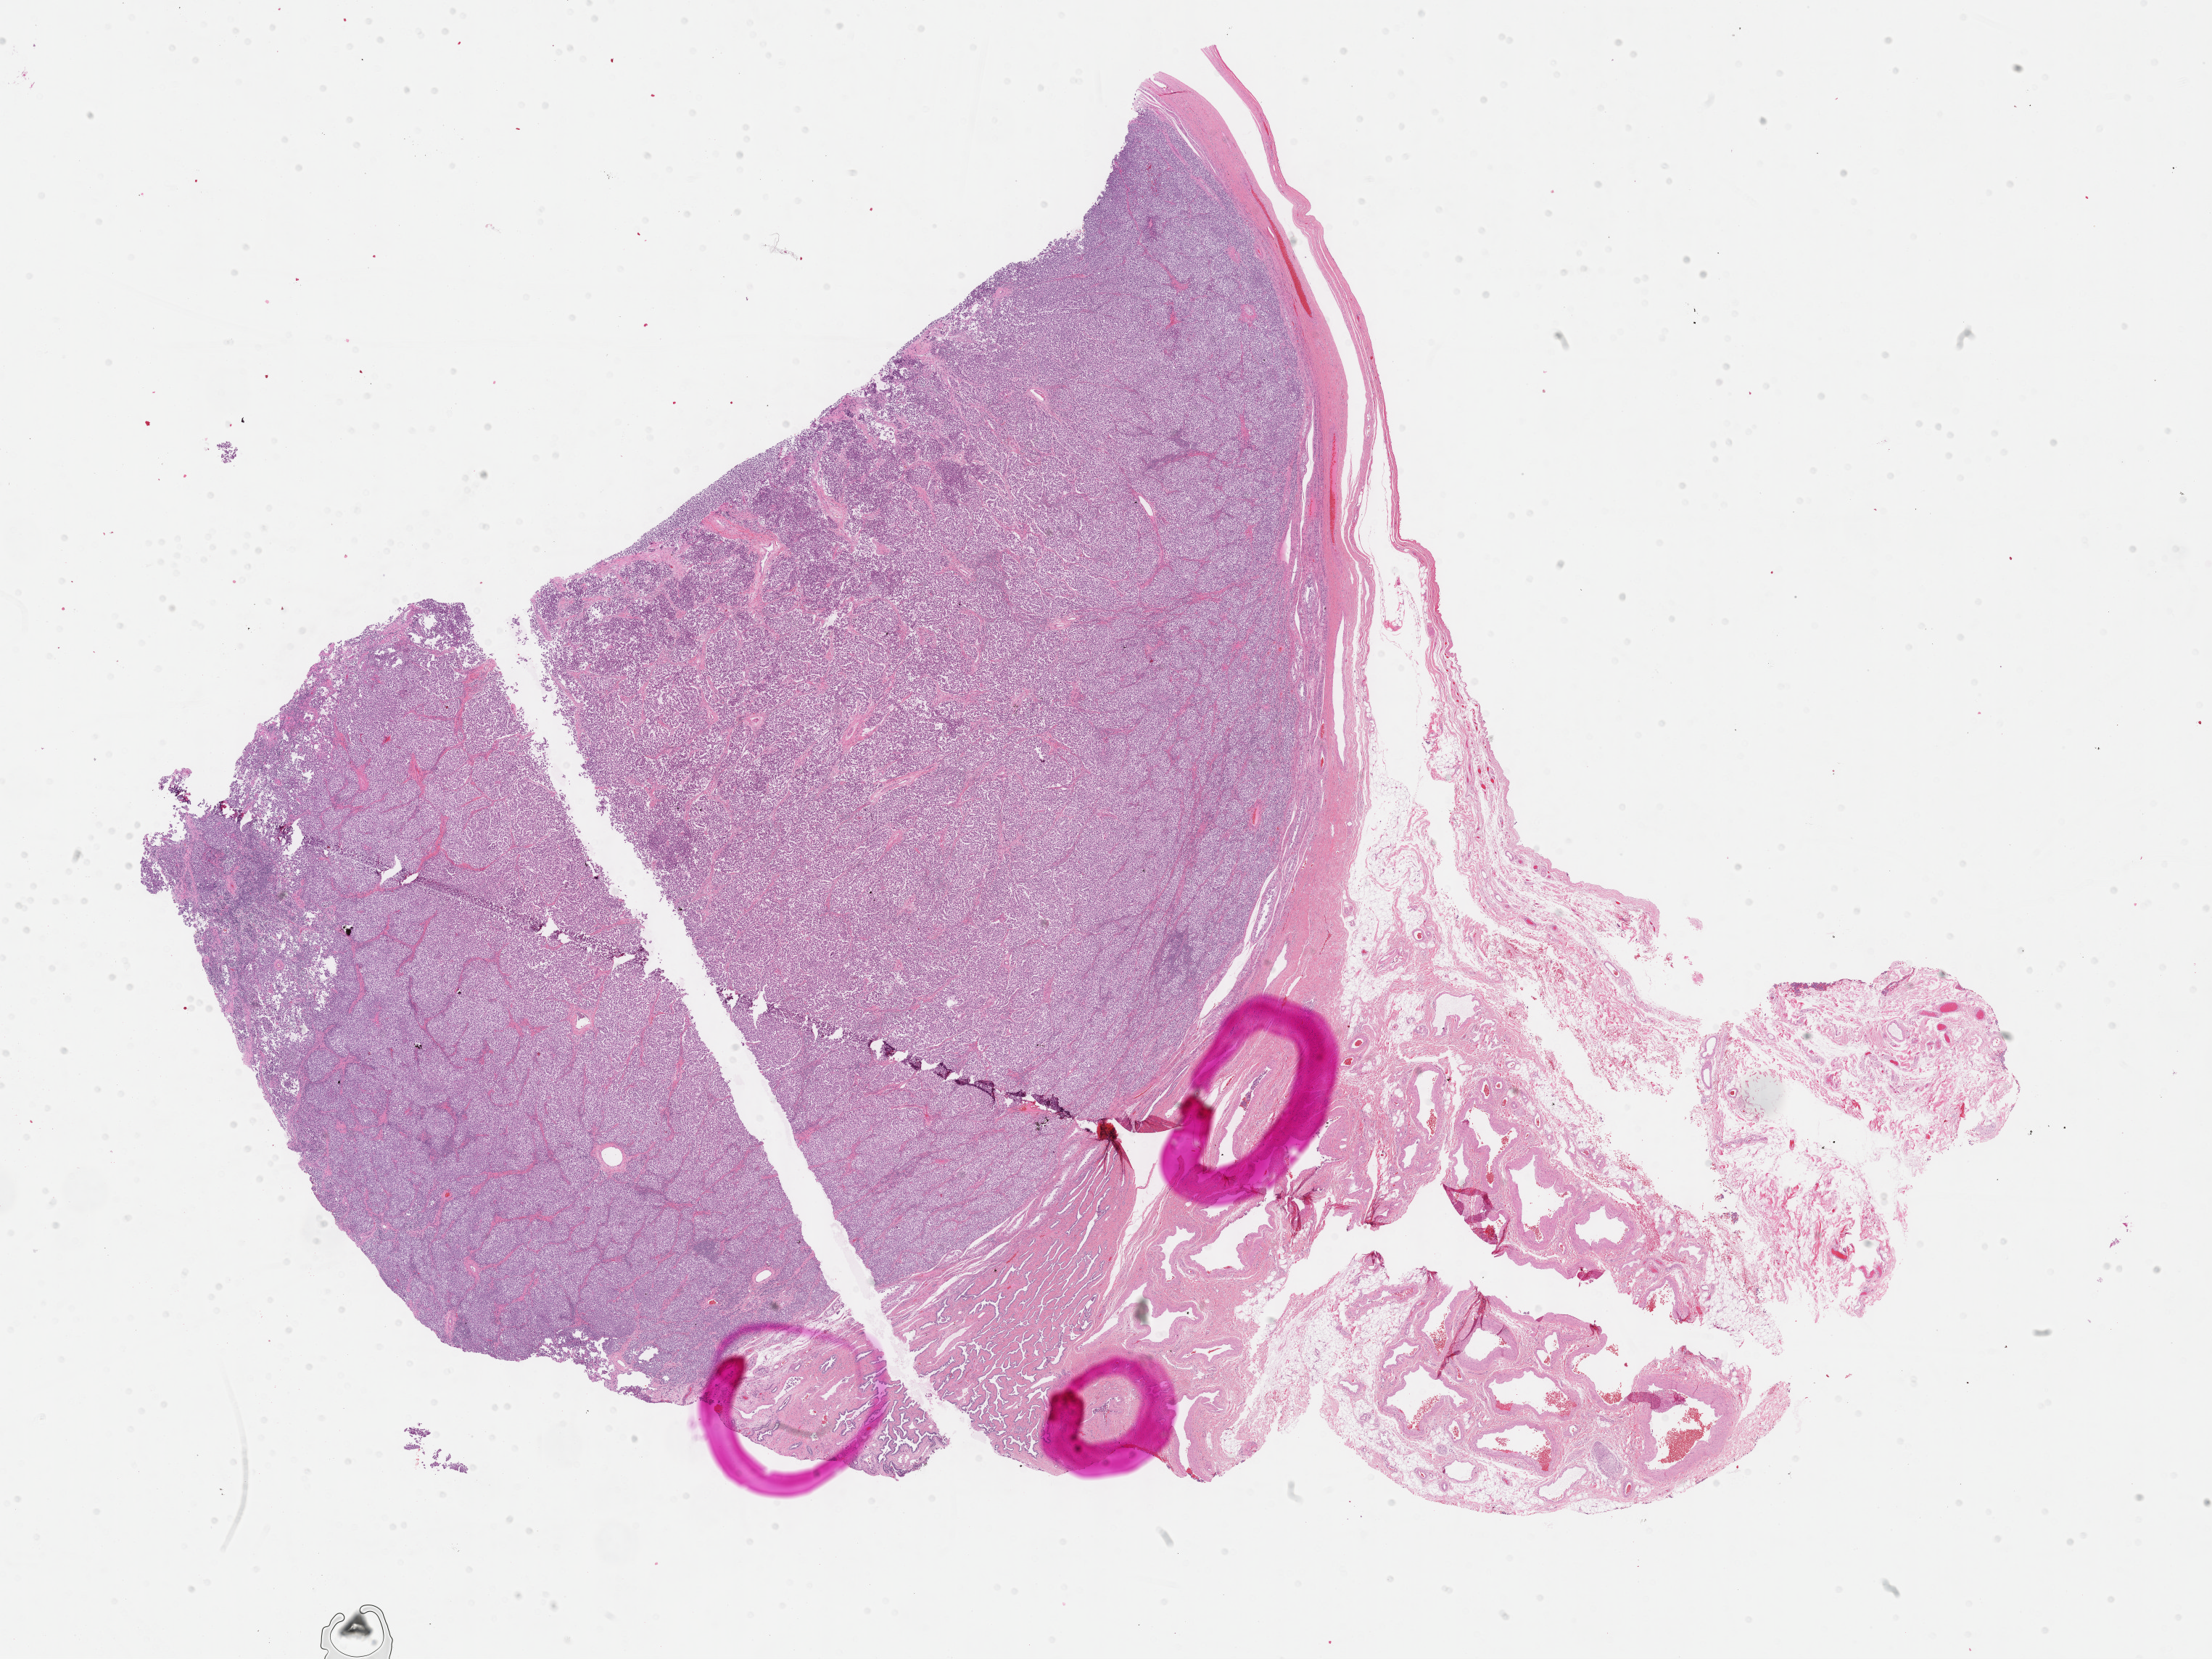
H&E whole-slide image, whole scanned area (about 24.7 x 18.5 mm, slide scanned at 40x) shown as a low-resolution overview. Formalin-fixed paraffin-embedded (FFPE) diagnostic section. Testis, primary tumour sample. Patient: male, age at initial diagnosis 38 years.
Pathologic diagnosis: Seminoma, NOS.